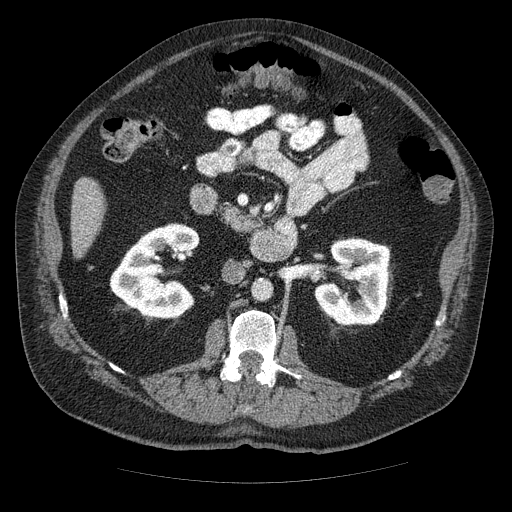
Contrast-enhanced abdominal CT (liver protocol), one axial slice. Position 9 of 85 along the scan axis. Reconstruction kernel STANDARD. 120 kVp. Soft-tissue window (W 400 / L 40 HU). 2.5 mm slice thickness. 512 × 512 image matrix, field of view 420 × 420 mm. From the clinical record (not read from this slice): diagnosis: hepatocellular carcinoma (patient treated with transarterial chemoembolisation; whether this scan precedes or follows treatment is not stated here); TNM stage (as recorded): Stage-IIIA; Child-Pugh class: A; tumour nodularity: multinodular.
Structures marked on this image (semi-automatically segmented with operator editing):
- liver parenchyma outside the tumour (the mass and vessels are separate outlines, so this box may not span the whole liver): box from (x=70, y=178) to (x=106, y=256) px